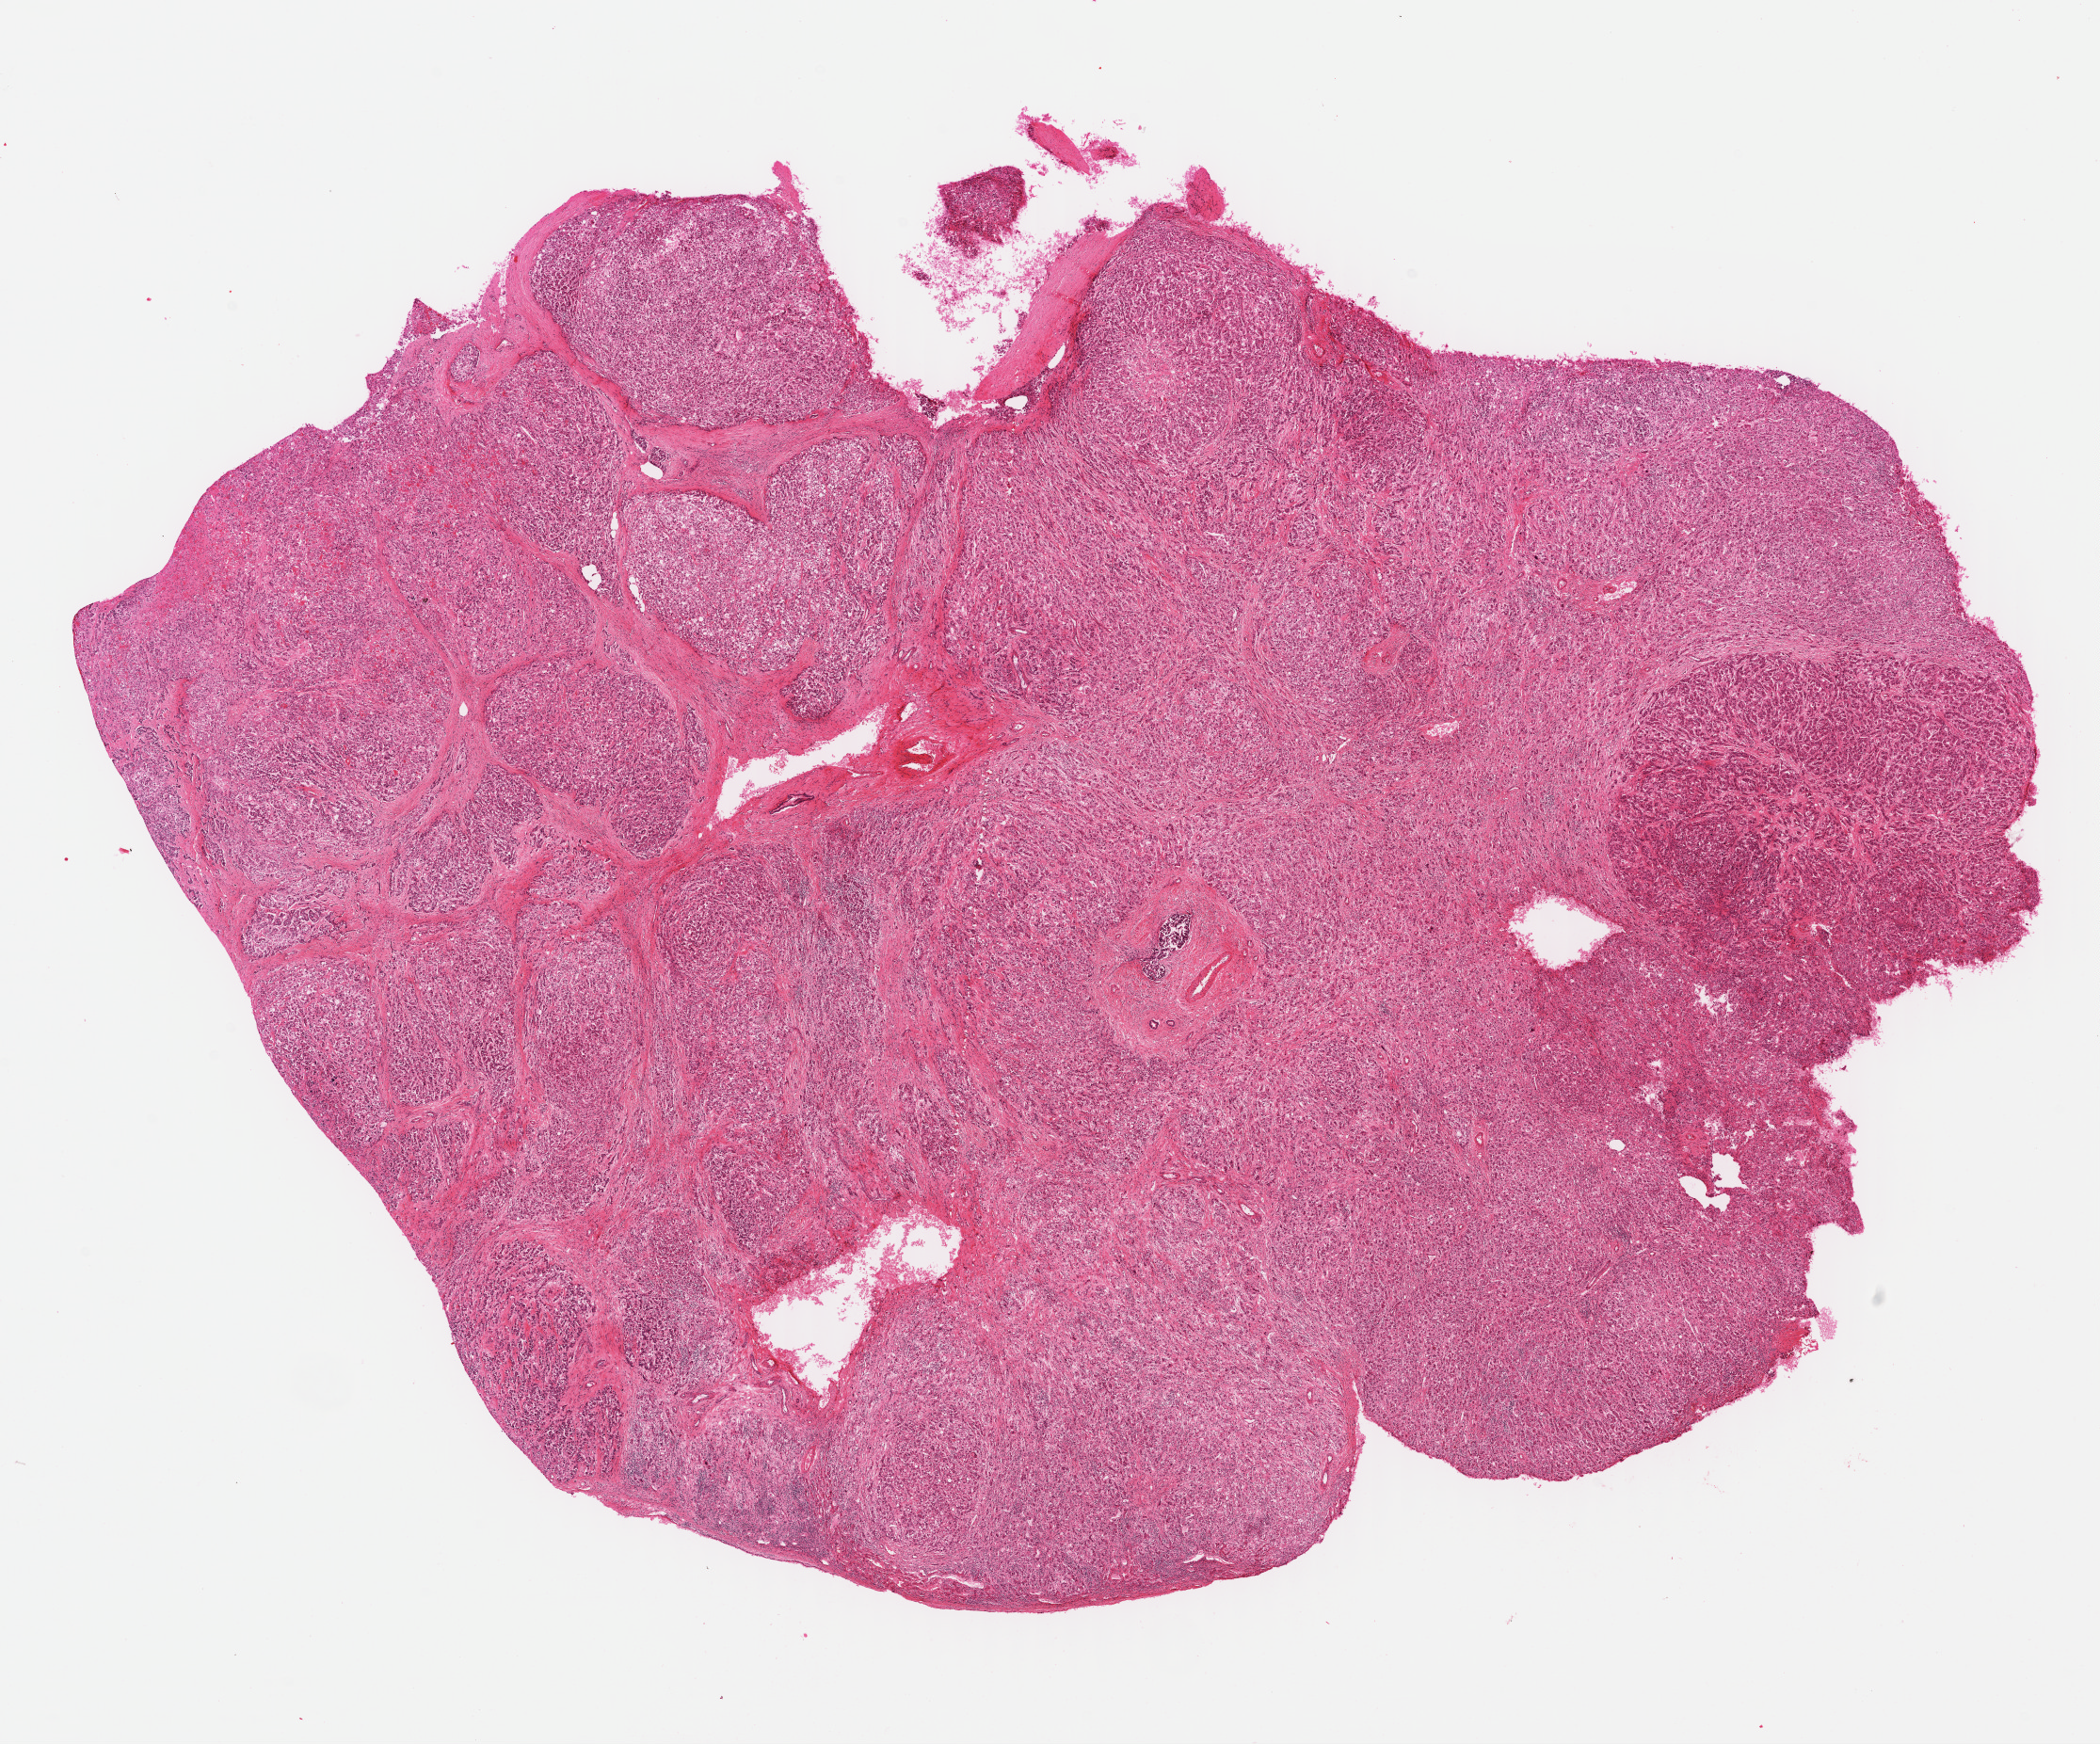
H&E-stained whole-slide image, a low-resolution overview of the entire scanned area, about 17.5 x 14.6 mm (acquisition: 40x scan), formalin-fixed paraffin-embedded (FFPE) diagnostic section, liver, primary tumour sample. Female patient; age at initial diagnosis 58 years. Histologic grade: G2 (moderately differentiated).
AJCC pathologic stage: IIIB. Histologic diagnosis: Hepatocellular carcinoma, NOS.